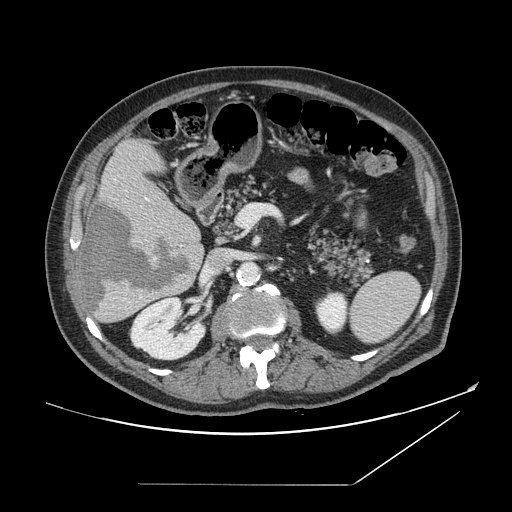
Contrast-enhanced abdominal CT, one axial slice; position 78 of 166 along the scan axis; soft-tissue window (W 400 / L 40 HU); 2.5 mm slice thickness; 512 × 512 image matrix, field of view 416 × 416 mm. Male patient, age 80 years. From the clinical record (not read from this slice): diagnosis: colorectal cancer liver metastases, imaged before liver resection; multiple liver metastases: no; largest metastasis: 2.2 cm; chemotherapy before resection: no.
Annotated regions visible in this slice (outlined manually by an expert reader):
- hepatic veins: bounding box <147,199,149,201> (left, top, right, bottom; pixels)
- liver: <79,140,205,324>
- planned liver remnant (the part of the liver to remain after resection): <102,140,198,233>
- liver metastasis: <83,200,191,317>